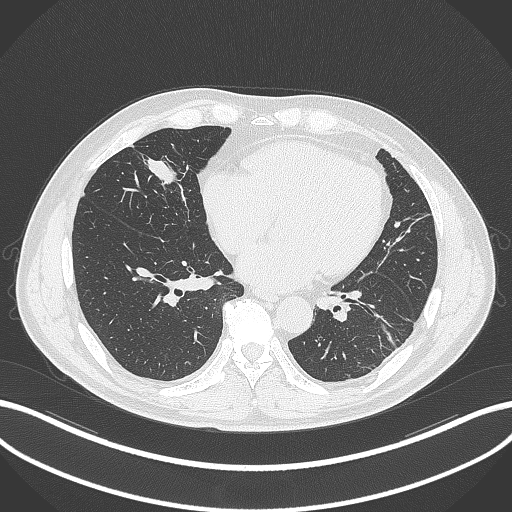
Chest CT, one axial slice; slice 103 of 399 in the series (ordered by position); reconstruction kernel B70f; 120 kVp; lung window (W 1500 / L -600 HU); 1 mm slice thickness; 512 × 512 image matrix, field of view 400 × 400 mm. Patient: male, 59 years. Case-level facts recorded for this patient, not image findings: clinical TNM (as recorded): T2a N1 M0.
Structures marked on this image (bounding box drawn by a radiologist):
- lung tumour (recorded histology: adenocarcinoma): bounding box (x1, y1, x2, y2) in pixels: (140, 150, 188, 191)